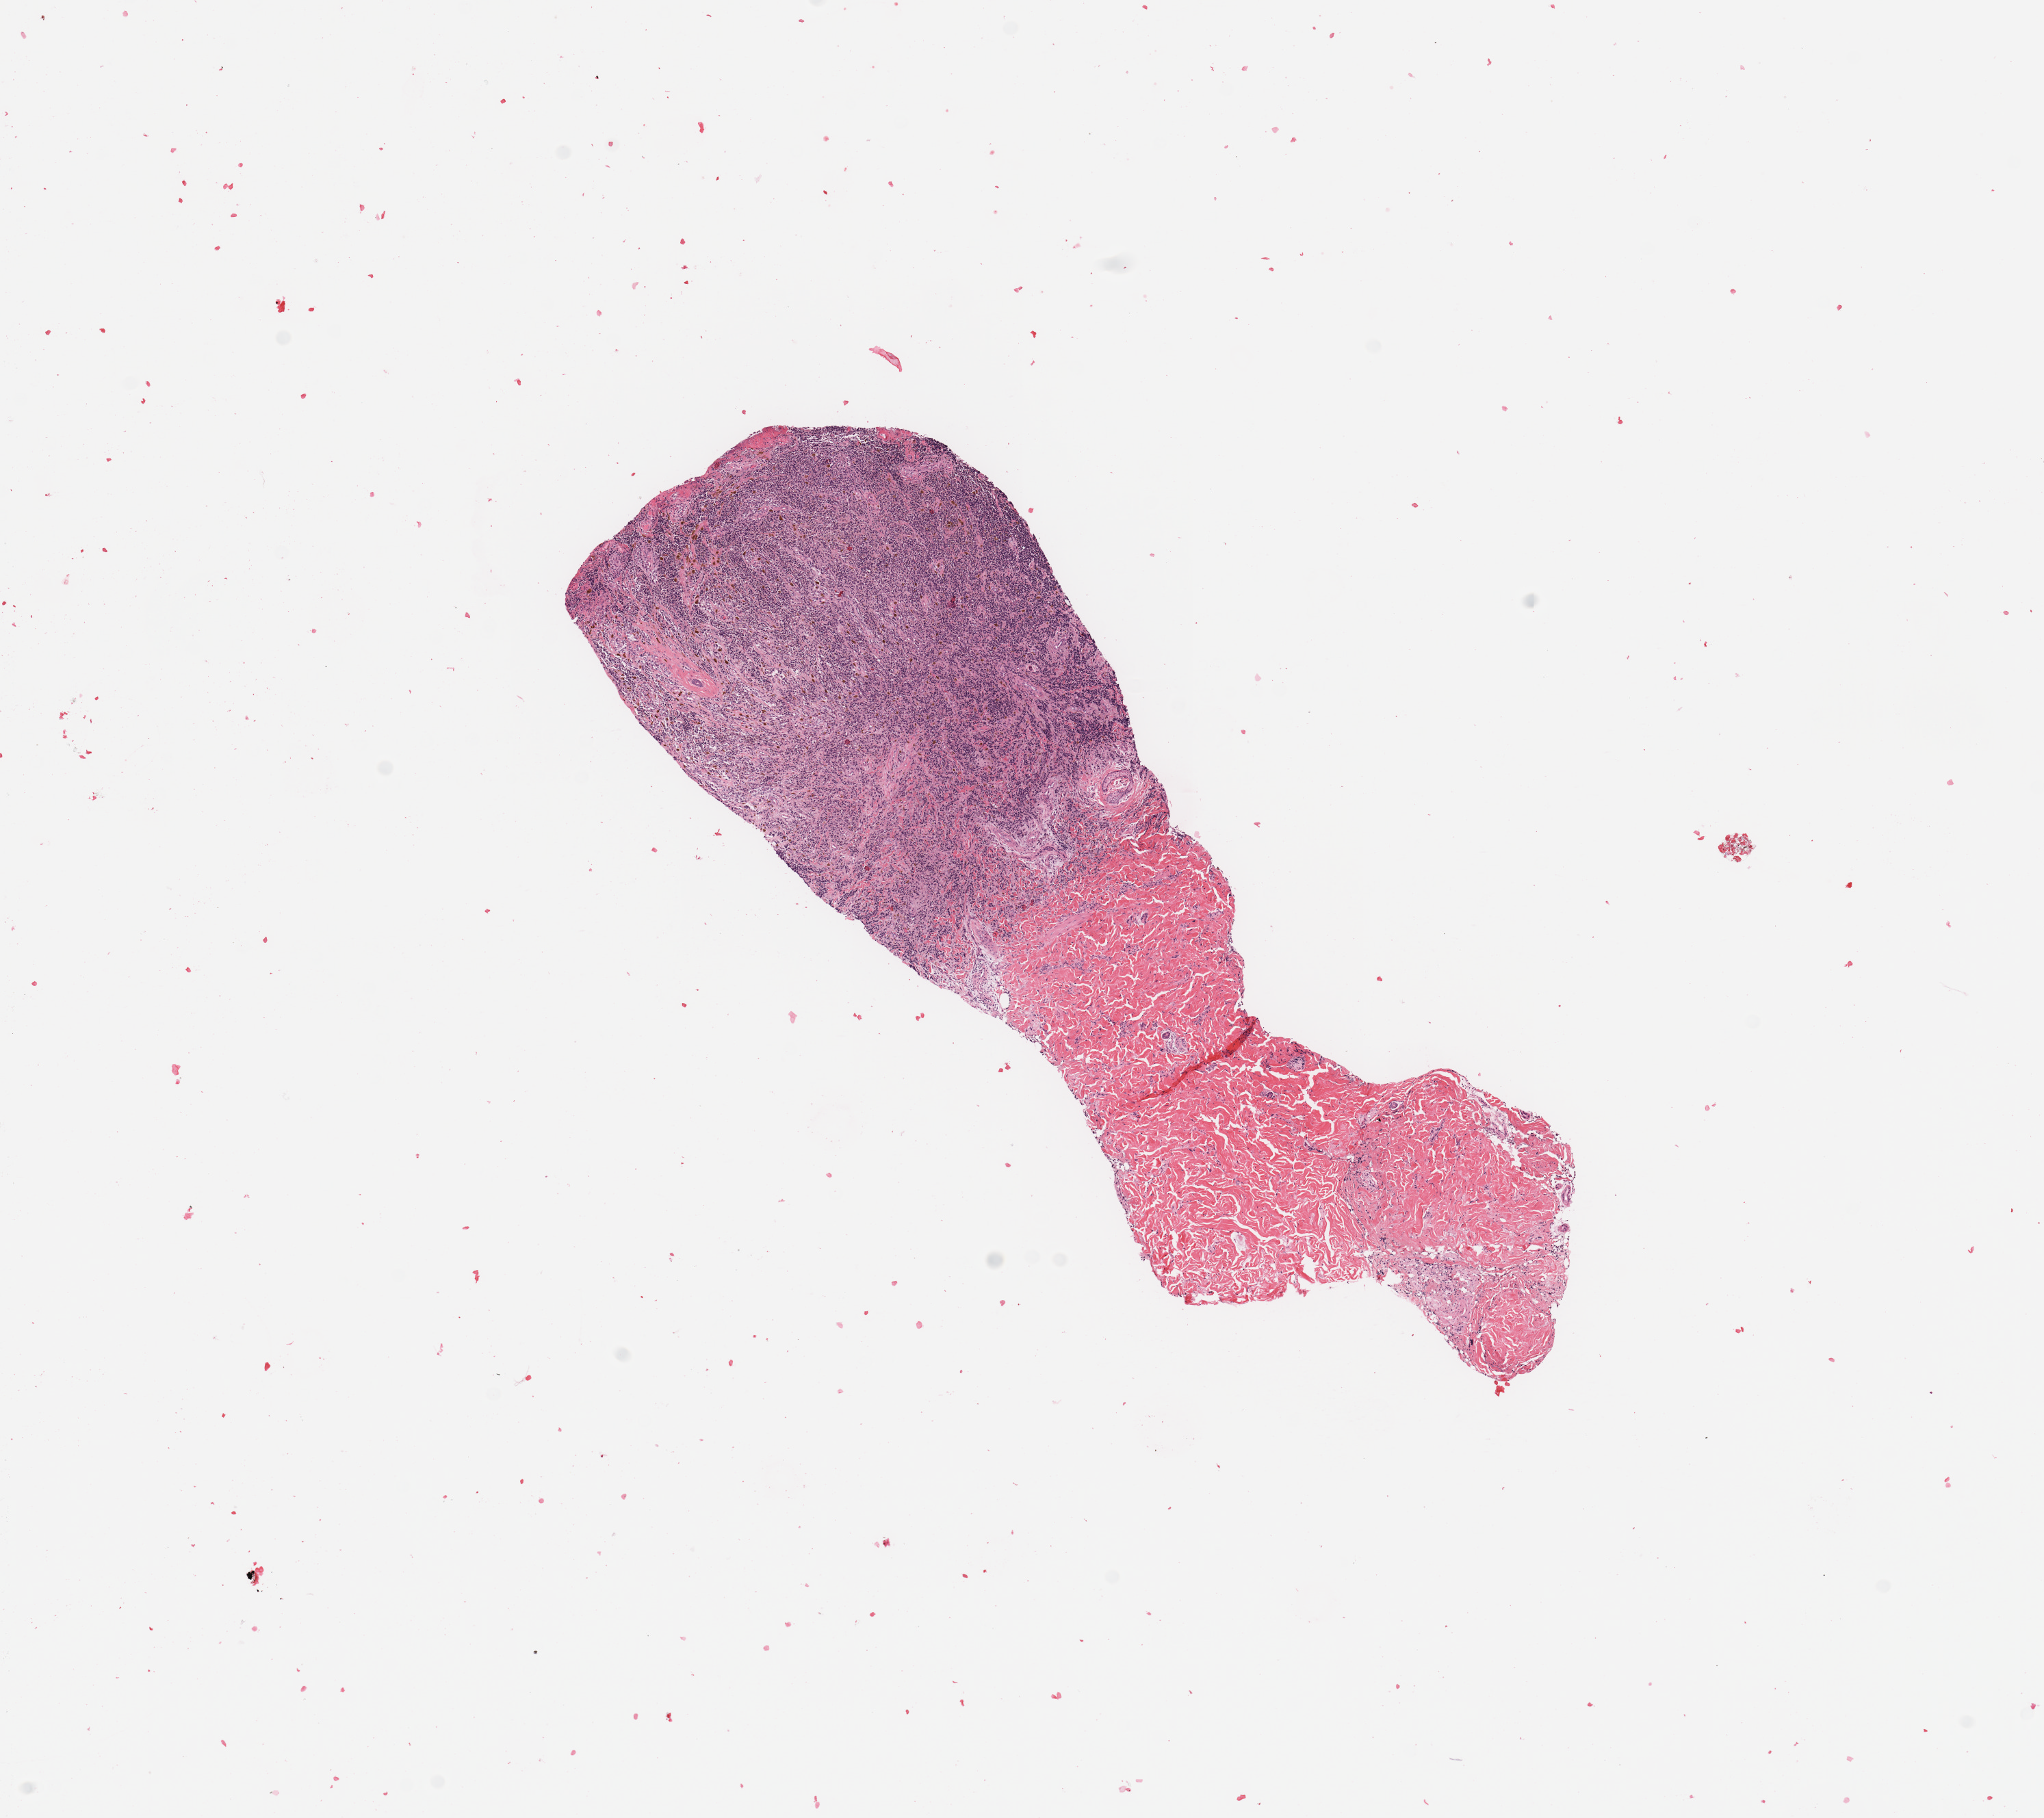
Whole-slide histology image, H&E — shown as a low-resolution overview of the whole scanned area (about 11.8 x 10.5 mm), tumour tissue sample, sampled site: skin. Patient: female, age 49 years. Composition of this section per pathologist review: tumour nuclei 85%, necrosis 0%.
Primary tumour site (as recorded): trunk. Diagnosis: Malignant melanoma, NOS.